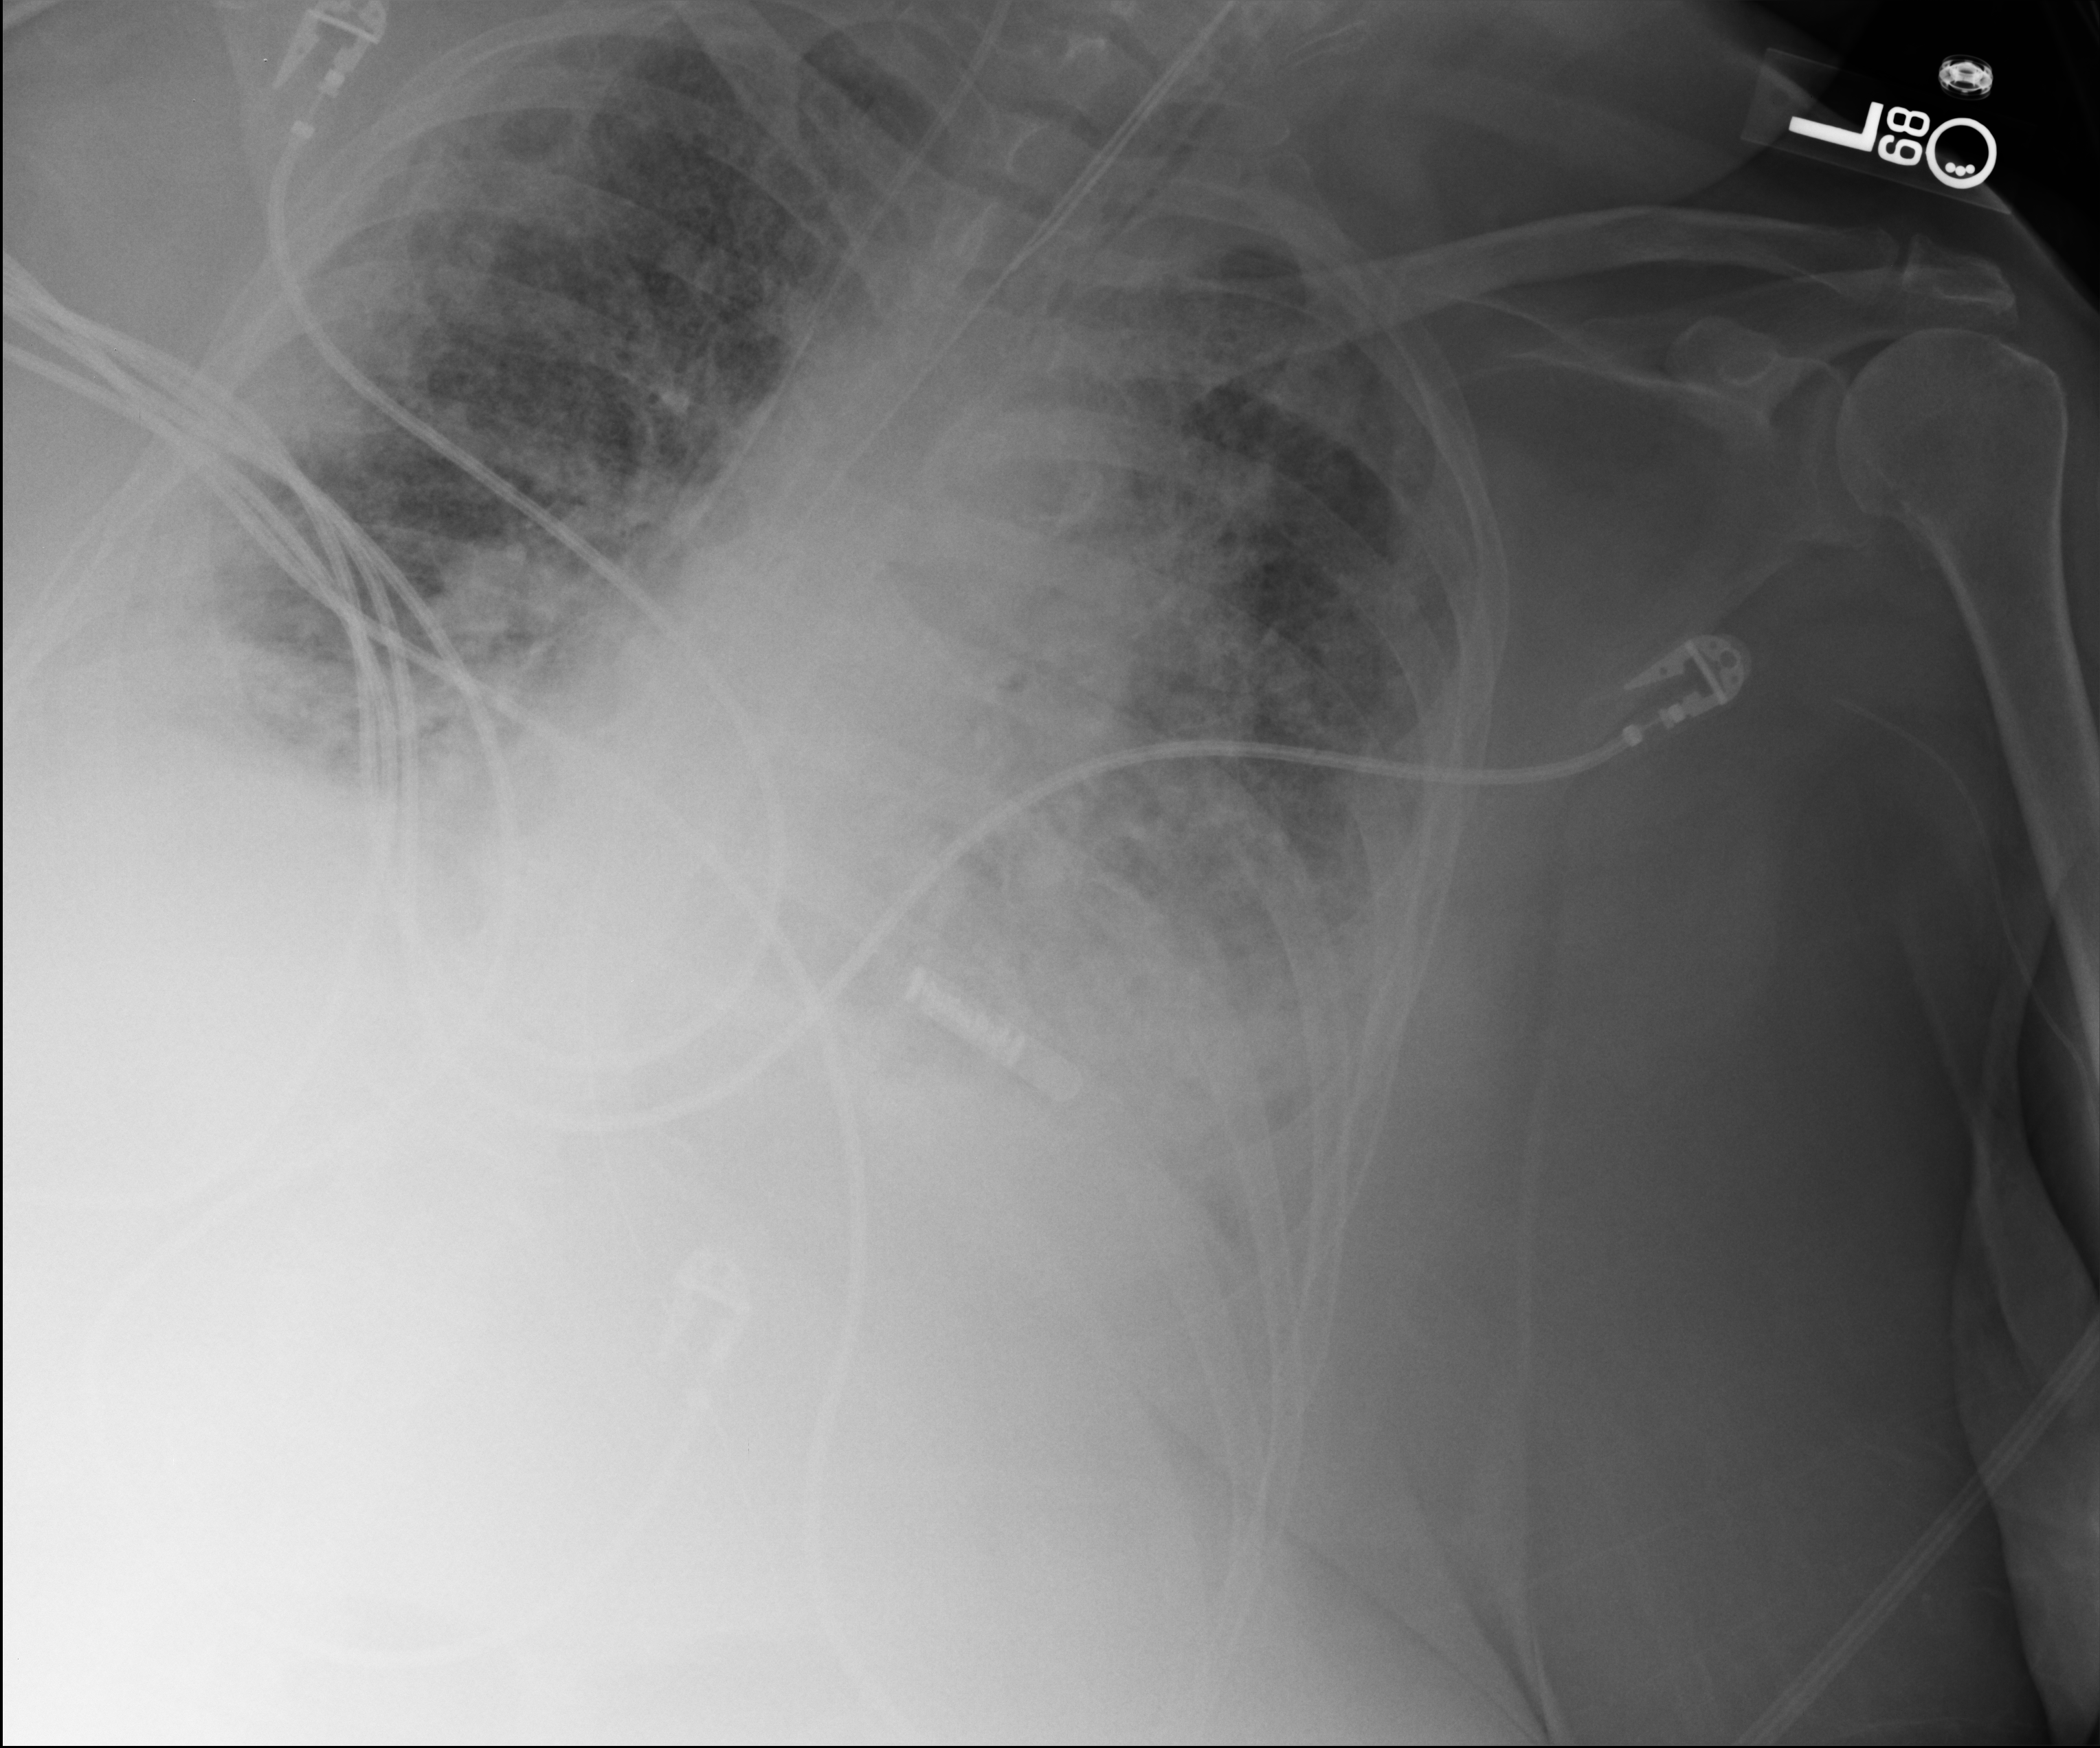
Bedside chest radiograph (computed radiography); anteroposterior (AP) projection. Patient hospitalised with COVID-19; female, aged 60–74 years.
Hospital-stay facts (about this admission, not read from this image; timing relative to this image not recorded): diabetes (admission record): yes; hypertension (admission record): yes.